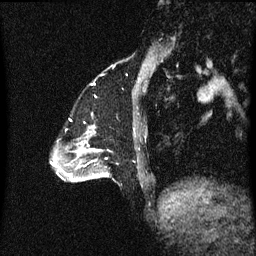
Breast MRI (dynamic contrast-enhanced), one sagittal slice; slice 15 of 60 in the series (ordered by position); dynamic contrast-enhanced series, image 2 of 3 at this slice position (ordered by acquisition); 1.5 T; TE 4.2 ms, TR 8.4 ms; 2 mm slice thickness; 256 × 256 image matrix. Patient: female, 47 years.
Structures marked on this image (semi-automatic segmentation, software-assisted and operator-edited):
- analysis volume of interest (the breast-tissue region the enhancement analysis was run in; not a lesion): bounding box [x1, y1, x2, y2] px = [85, 136, 115, 181]
- tumour enhancement mask (voxels above the 70 % enhancement threshold inside the analysis volume of interest): [93, 150, 102, 177]